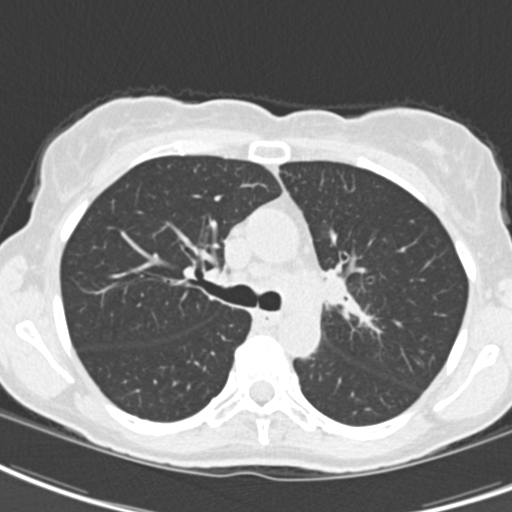
Low-dose screening chest CT, one axial slice; position 132 of 189 along the scan axis; reconstruction kernel B30f; lung window (W 1500 / L -600 HU); 2 mm slice thickness; 512 × 512 image matrix, field of view 279 × 279 mm.
Structures marked on this image (manually delineated by an expert):
- lesion 2 (tumor, hilum of left lung): bounding box (x1, y1, x2, y2) in pixels: (322, 272, 346, 304)